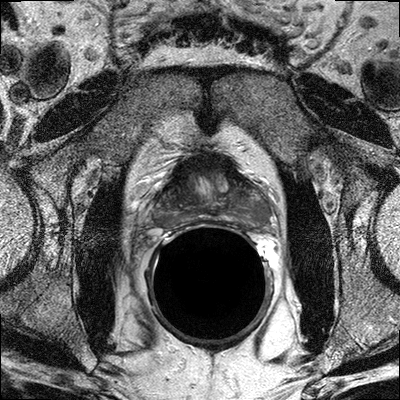
MRI of the prostate; 3 images, each a single mid-volume slice chosen by position (not for content). Treatment context recorded for this patient: Surgery.
Image 1: axial T2-weighted image, series "T2W_TSE_AX", slice 19 of 36.
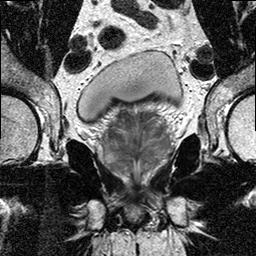
Image 2: T2-weighted coronal slice, slice 13 of 24, 3 mm slice thickness.
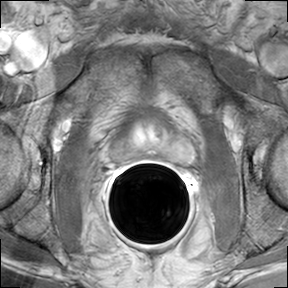
Image 3: DCE (dynamic gadolinium-enhanced) axial slice, series "AX BLISS_GAD", slice 18 of 34, dynamic phase 4 of 7.
Report of this MRI examination:
prostate has a maximal lateral diameter of 4.8 cm, a maximal craniocaudal diameter of 4.3 cm and a maximal AP diameter of 2.2 cm resulting in an estimated gland volume of 25 cc. The zonal anatomy is preserved There is a T2-w hypointense nodule seen in the left base/midthird measuring 11 x 7 x 15 mm, in the posterior lateral peripheral zone at 4-6 o'clock. There is associated suspicious enhancement. This is highly suspicious for prostate cancer. The adjacent "capsule" shows also increased enhancement, which suggests capsular infiltration. No manifest tumor mass seen beyond the capsule. No evidence for involvement of the neurovascular bundle on either side. No evidence for seminal vesicles infiltration. No evidence of involvement of bladder neck and rectal wall. No suspiciously enlarged obturator and iliac lymph nodes. (bilateral <5 mm iliac lymph nodes) Multiplanar reconstructions, subtraction images, and CAD analysis of the dynamic series for assessment of the kinetic information facilitated the interpretation of the exam. IMPRESSION: 1) 1.5 cm tumor in the left posterior lateral peripheral zone, with dominant nodule in base and midthird, with capsular infiltration, however, there are no manifest tumor masses beyond the capsule seen. 2) No evidence for right sided tumor. 3) No evidence of seminal vesicle infiltration or lymphadenopathy.

Prostatectomy specimen pathology (as recorded; the surgery followed this MRI):
Radical prostatectomy Prostate Size: Weight: 51.4 g Size: 5X4.5X4.0cm Lymph Node Sampling Pelvic lymph node dissection Histologic Type : Adenocarcinoma (acinar, not otherwise specified) Histologic Grade Gleason Pattern Primary Pattern: Grade 3 Secondary Pattern: Grade 4 Total Gleason Score: 3+4=7/10 Tumor Quantitation: Proportion (percentage) of prostate involved by tumor: 20% Extraprostatic Extension: Present, focal (left anterior lobe at the base) Seminal Vesicle Invasion: Not identified Margins: Margins uninvolved by invasive carcinoma Treatment Effect on Carcinoma: Not identified Lymph-Vascular Invasion: Not identified Perineural Invasion: Present Pathologic Staging (pTNM): Primary Tumor (pT) pT3a Extraprostatic extension or microscopic invasion of bladder neck Regional Lymph Nodes (pN) pN0: No regional lymph node metastasis Specify: Number examined: 26 Number involved: 0 Distant Metastasis (pM) Not applicable Pathologic Staging pT3a pN0 pMx *Additional Pathologic Findings High-grade prostatic intraepithelial neoplasia (PIN) B. PORTION OF LEFT SEMINAL VESICLE: FIBROVASCULAR AND FIBROADPISE TISSUE. NO SEMINAL VESICLE TISSUE IDENTIFIED (ENTIRE SPECIMEN SUBMITTED FOR HISTOLOGICAL EXAMINATION) NO TUMOR IDENTIFIED. C. RIGHT EXTERNAL ILIAC LYMPH NODES: EIGHT (8) REACTIVE LYMPH NODES, NO TUMOR IDENTIFIED. Addendum Diagnosis IMMUNOSTAIN FOR AE1/AE3 PERFORMED ON BLOCK C1 IS NEGATIVE. IMMUNOSTAIN FOR AE1/AE3 WILL BE EXAMINED AND RESULTS REPORTED IN AN ADDENDUM. D. RIGHT OBTURATOR LYMPH NODES: SEVEN (7) REACTIVE LYMPH NODES, NO TUMOR IDENTIFIED. E. LEFT EXTERNAL ILIAC LYMPH NODES: FIVE (5) REACTIVE LYMPH NODES, NO TUMOR IDENTIFIED. F. LEFT OBTURATOR LYMPH NODES: SIX (6) REACTIVE LYMPH NODES, NO TUMOR IDENTIFIED. G. RIGHT SEMINAL VESICLE: SEMINAL VESICLE TISSUE. NO TUMOR IDENTIFIED. Addendum Diagnosis IMMUNOSTAIN FOR AE1/AE3 PERFORMED ON BLOCK C1 IS NEGATIVE.